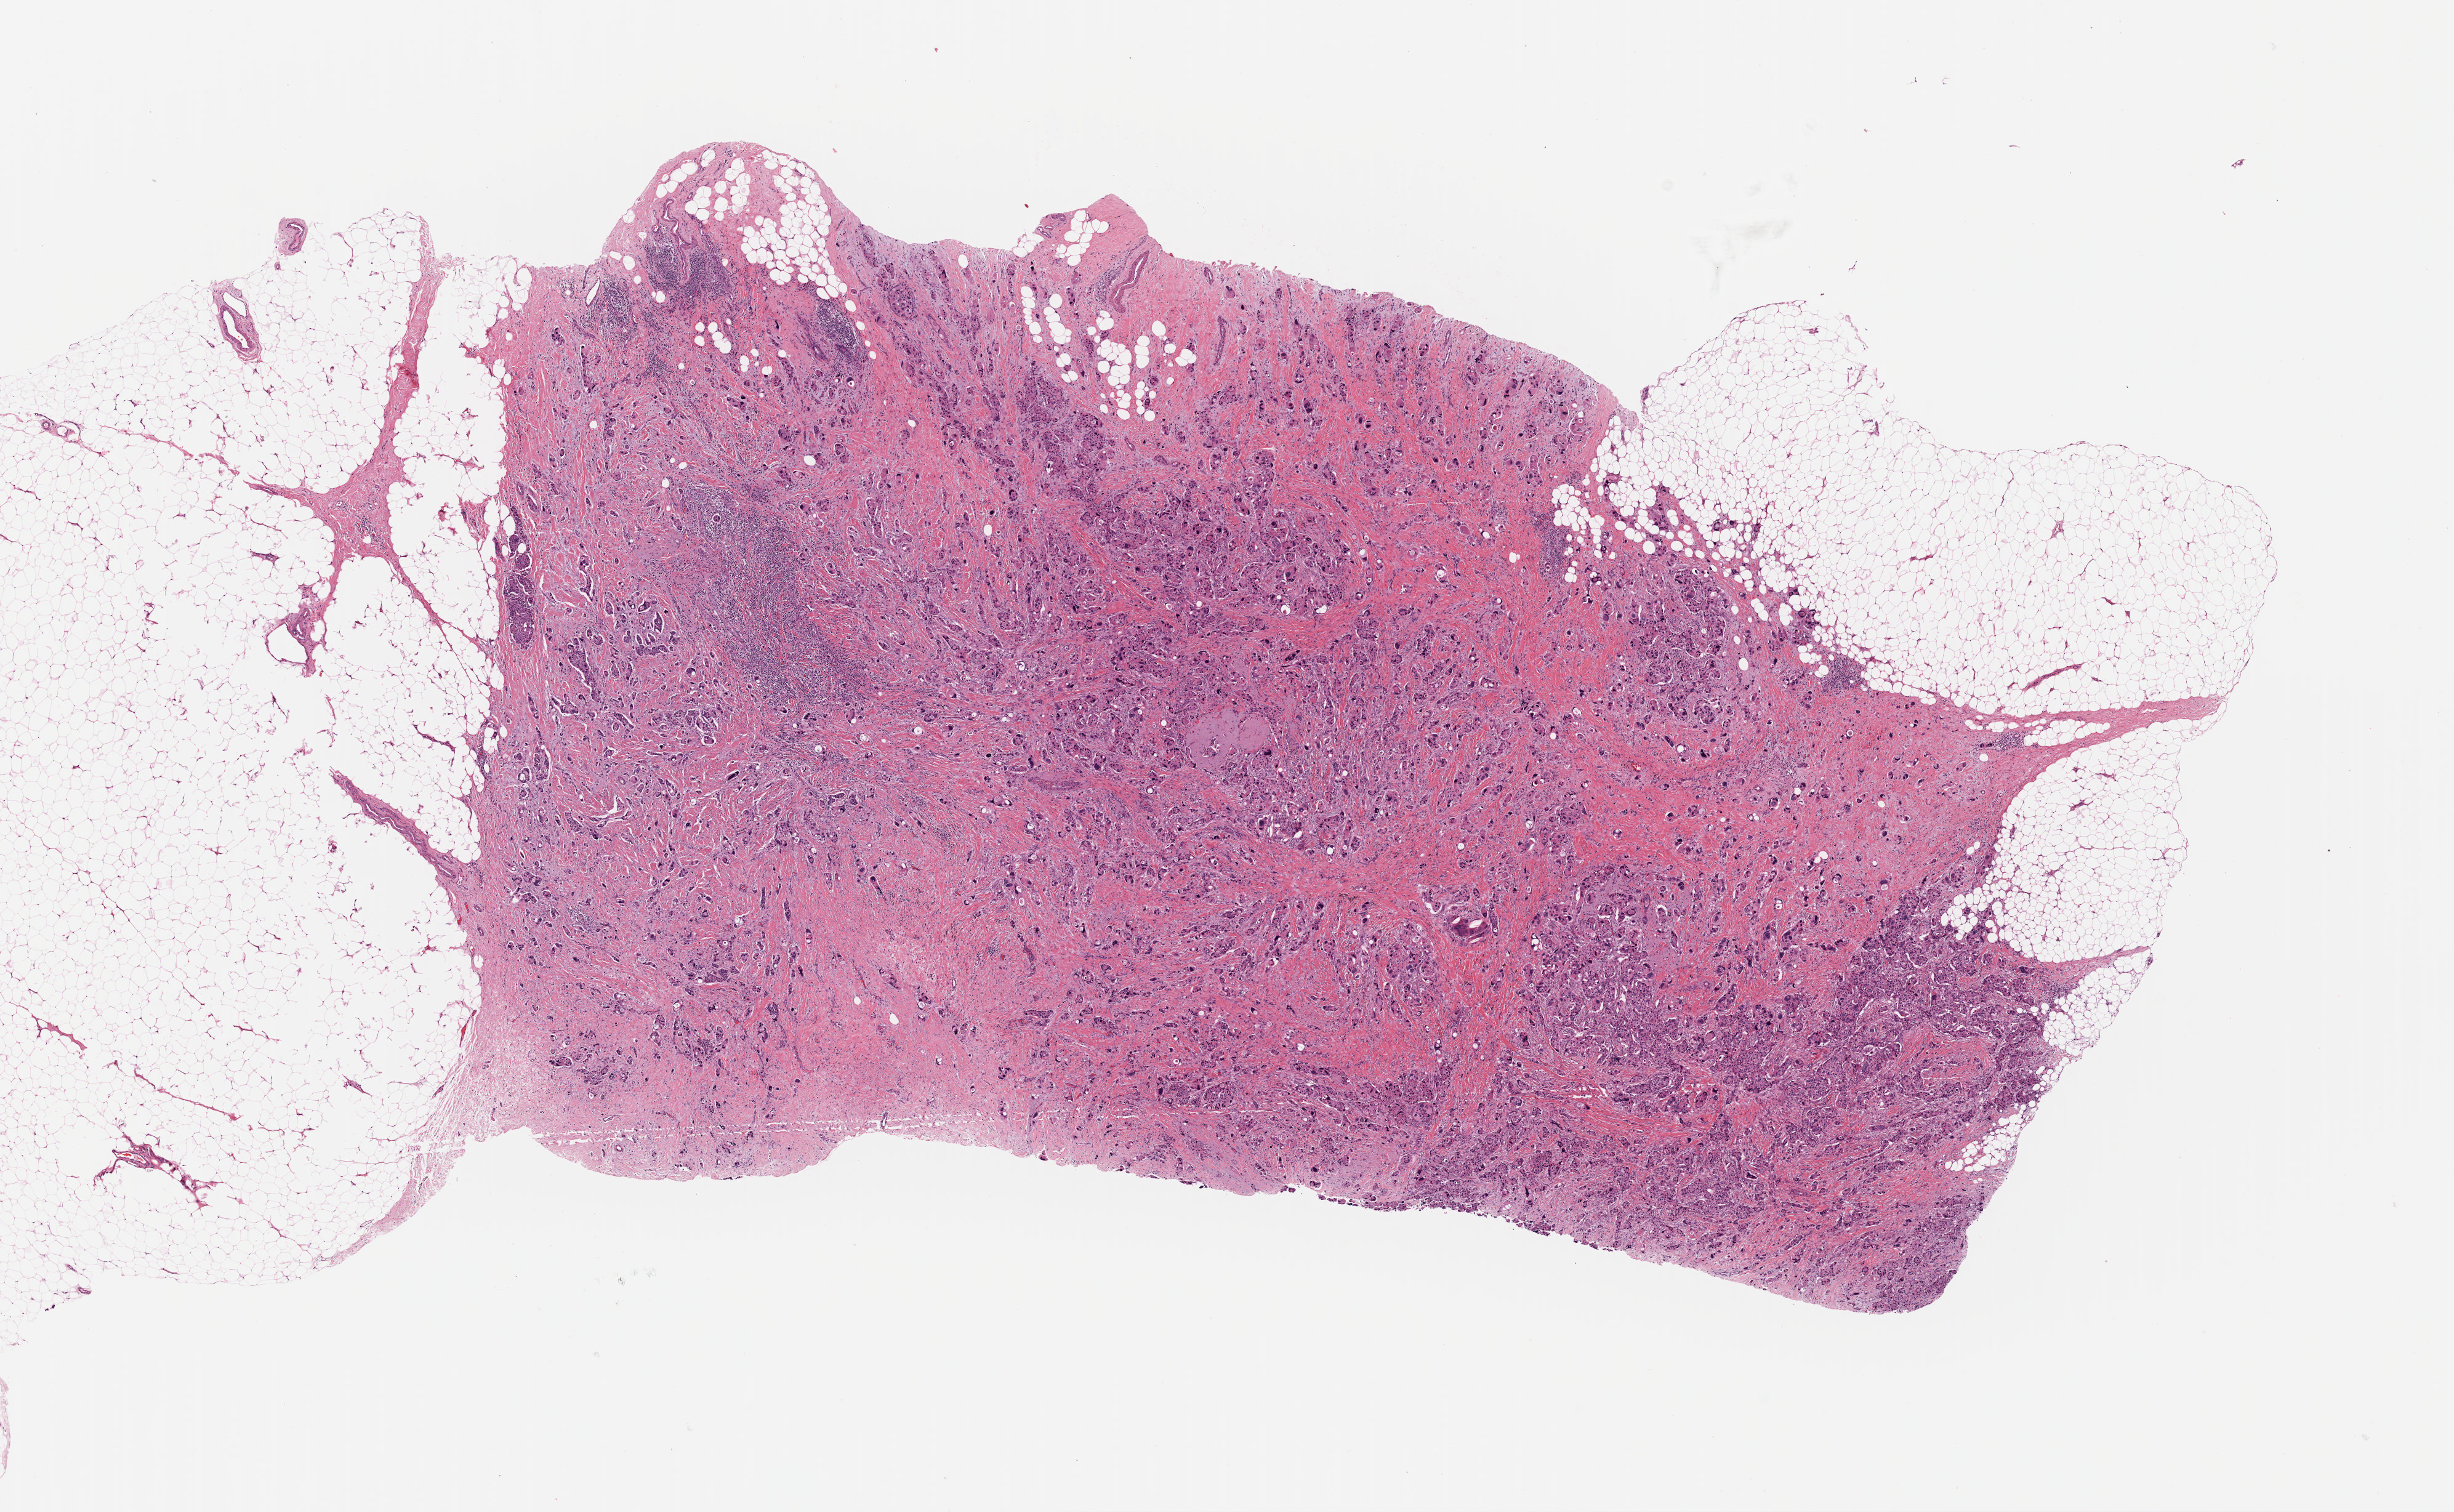
H&E-stained whole-slide image — shown as a low-resolution overview of the whole scanned area (about 15.7 x 9.7 mm, from a 40x scan), FFPE section, primary tumour sample from the breast. Patient: female, age at initial diagnosis 63 years.
Pathologic diagnosis: Infiltrating duct carcinoma, NOS.